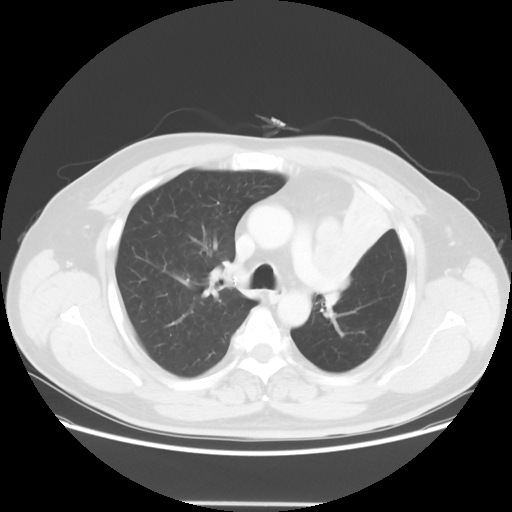
Chest CT, one axial slice. Reconstruction kernel STANDARD. Lung window (W 1500 / L -600 HU). 5 mm slice thickness. 512 × 512 image matrix, field of view 403 × 403 mm. Male patient, age 49 years. Case-level facts recorded for this patient, not image findings: clinical TNM (as recorded): T3 N3 M1c.
Structures marked on this image (bounding box drawn by a radiologist):
- lung tumour (recorded histology: squamous cell carcinoma): bounding box [x1, y1, x2, y2] px = [304, 214, 364, 318]